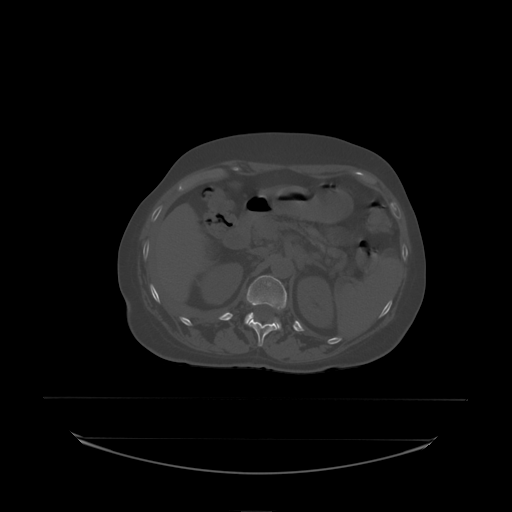
CT including the spine, one axial slice; slice 89 of 242 in the series (ordered by position); bone window (W 1800 / L 400 HU); 2.5 mm slice thickness; 512 × 512 image matrix. Female patient, age 53 years. Case-level facts recorded for this patient, not image findings: primary cancer: lung; vertebrae with lytic lesions (as recorded): T7, L1.
Outlined on this slice (semi-automatic segmentation, software-assisted and operator-edited):
- L1 vertebra: bounding box [x1, y1, x2, y2] px = [245, 276, 287, 331]
- T12 vertebra: [249, 318, 278, 338]